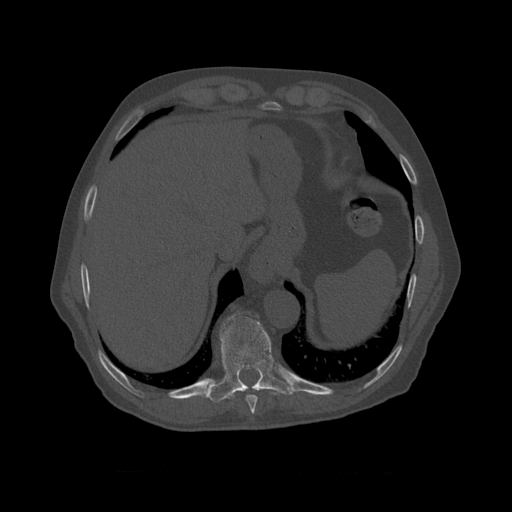
CT including the spine, one axial slice; slice 429 of 450 in the series (ordered by position); bone window (W 1800 / L 400 HU); 1.25 mm slice thickness; 512 × 512 image matrix, field of view 405 × 405 mm. Patient age 75 years. Case-level facts recorded for this patient, not image findings: primary cancer: prostate.
Structures marked on this image (semi-automatically segmented with operator editing):
- T8 vertebra: box from (x=246, y=395) to (x=258, y=410) px
- T9 vertebra: (x=213, y=312)–(x=293, y=400)